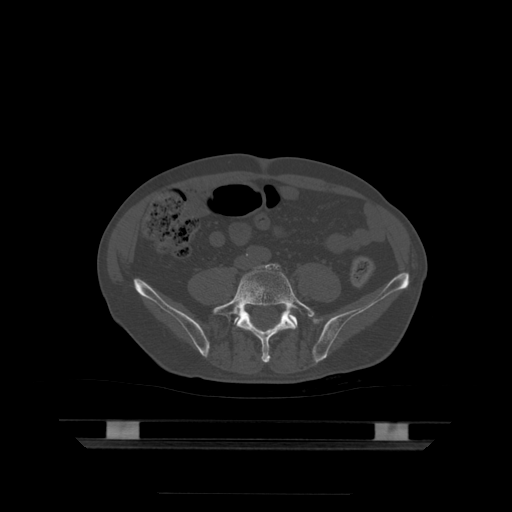
CT including the spine, one axial slice; slice 73 of 522 in the series (ordered by position); bone window (W 1800 / L 400 HU); 1.25 mm slice thickness; 512 × 512 image matrix, field of view 436 × 436 mm. Patient age 68 years. Case-level facts recorded for this patient, not image findings: primary cancer: urothelial.
Structures marked on this image (semi-automatic segmentation, software-assisted and operator-edited):
- L5 vertebra: bounding box (x1, y1, x2, y2) in pixels: (213, 264, 315, 363)